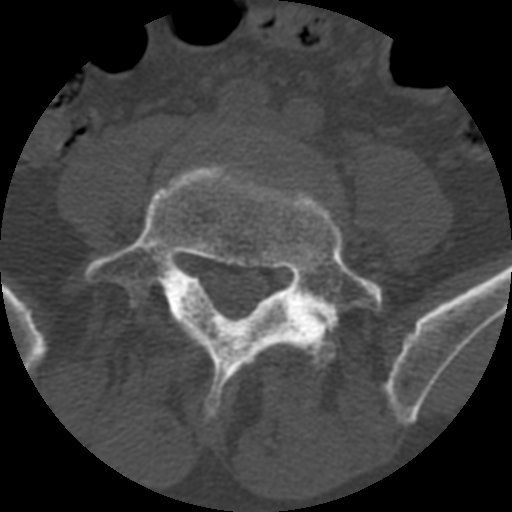
CT including the spine, one axial slice; slice 259 of 399 in the series (ordered by position); reconstruction kernel STANDARD; 120 kVp; bone window (W 1800 / L 400 HU); 1.25 mm slice thickness; 512 × 512 image matrix. Patient age 71 years. Case-level facts recorded for this patient, not image findings: primary cancer: prostate.
Annotated regions visible in this slice (semi-automatically segmented with operator editing):
- L5 vertebra: box from (x=83, y=162) to (x=384, y=424) px